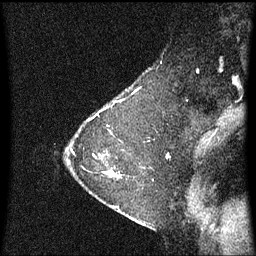
Breast MRI (dynamic contrast-enhanced), one sagittal slice; position 47 of 60 along the scan axis; dynamic contrast-enhanced series, image 2 of 3 at this slice position (ordered by acquisition); 1.5 T; TE 4.2 ms, TR 8.4 ms; 256 × 256 image matrix, field of view 200 × 200 mm. Female patient, age 36 years. From the clinical record (not read from this slice): setting: breast cancer imaged before/during neoadjuvant chemotherapy; receptor status: HR-positive, HER2-negative.
Annotated regions visible in this slice (semi-automatically segmented with operator editing):
- analysis volume of interest (the breast-tissue region the enhancement analysis was run in; not a lesion): bounding box (x1, y1, x2, y2) in pixels: (72, 118, 123, 185)
- tumour enhancement mask (voxels above the 70 % enhancement threshold inside the analysis volume of interest): (110, 172, 113, 175)